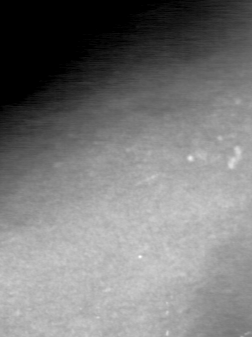
Region of interest cut from a scanned film mammogram (one marked finding); right breast; CC view.
Finding: calcifications, morphology pleomorphic, distribution clustered; BI-RADS assessment category 3; pathology result (as recorded, not read from the image): malignant.